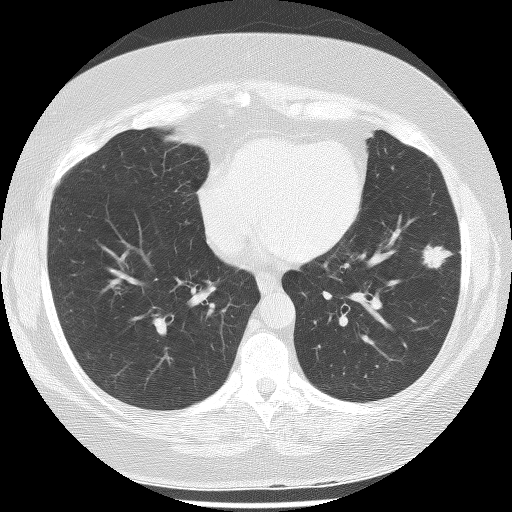
Low-dose screening chest CT, axial slice; baseline annual screen; lung window (W 1500 / L -600 HU); 2.5 mm slice thickness; lung (sharp) reconstruction kernel (BONE); slice 132 of 233 in the series; 512 × 512 image matrix. Female participant, aged 56 years at enrolment. Former smoker at enrolment.
• Expert reader's lesion annotation, box from (x=393, y=226) to (x=463, y=284) px.
• Reader record for this screening exam (exam-level; its link to the box is not recorded): non-calcified nodule or mass ≥4 mm, left lower lobe, 22 × 17 mm, spiculated (stellate) margins, soft tissue attenuation.
• Participant outcome: lung cancer diagnosed 63 days after this screen — bronchiolo-alveolar adenocarcinoma, NOS, left lower lobe, stage IA (AJCC 6th edition), 18 mm at pathology.